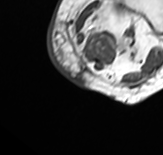
MRI of an extremity soft-tissue mass, one axial slice; position 1 of 65 along the scan axis; MR volume resampled by the dataset authors to the PET/CT grid (not the native acquisition matrix); 3.27 mm slice thickness; 163 × 155 image matrix. Female patient. From the clinical record (not read from this slice): histological type: pleomorphic leiomyosarcoma; grade: high; site of the primary tumour: left thigh.
Annotated regions visible in this slice (expert contour drawn on MRI and transferred to this co-registered scan by the dataset authors):
- gross tumour volume including surrounding oedema: bounding box <71,0,138,66> (left, top, right, bottom; pixels)